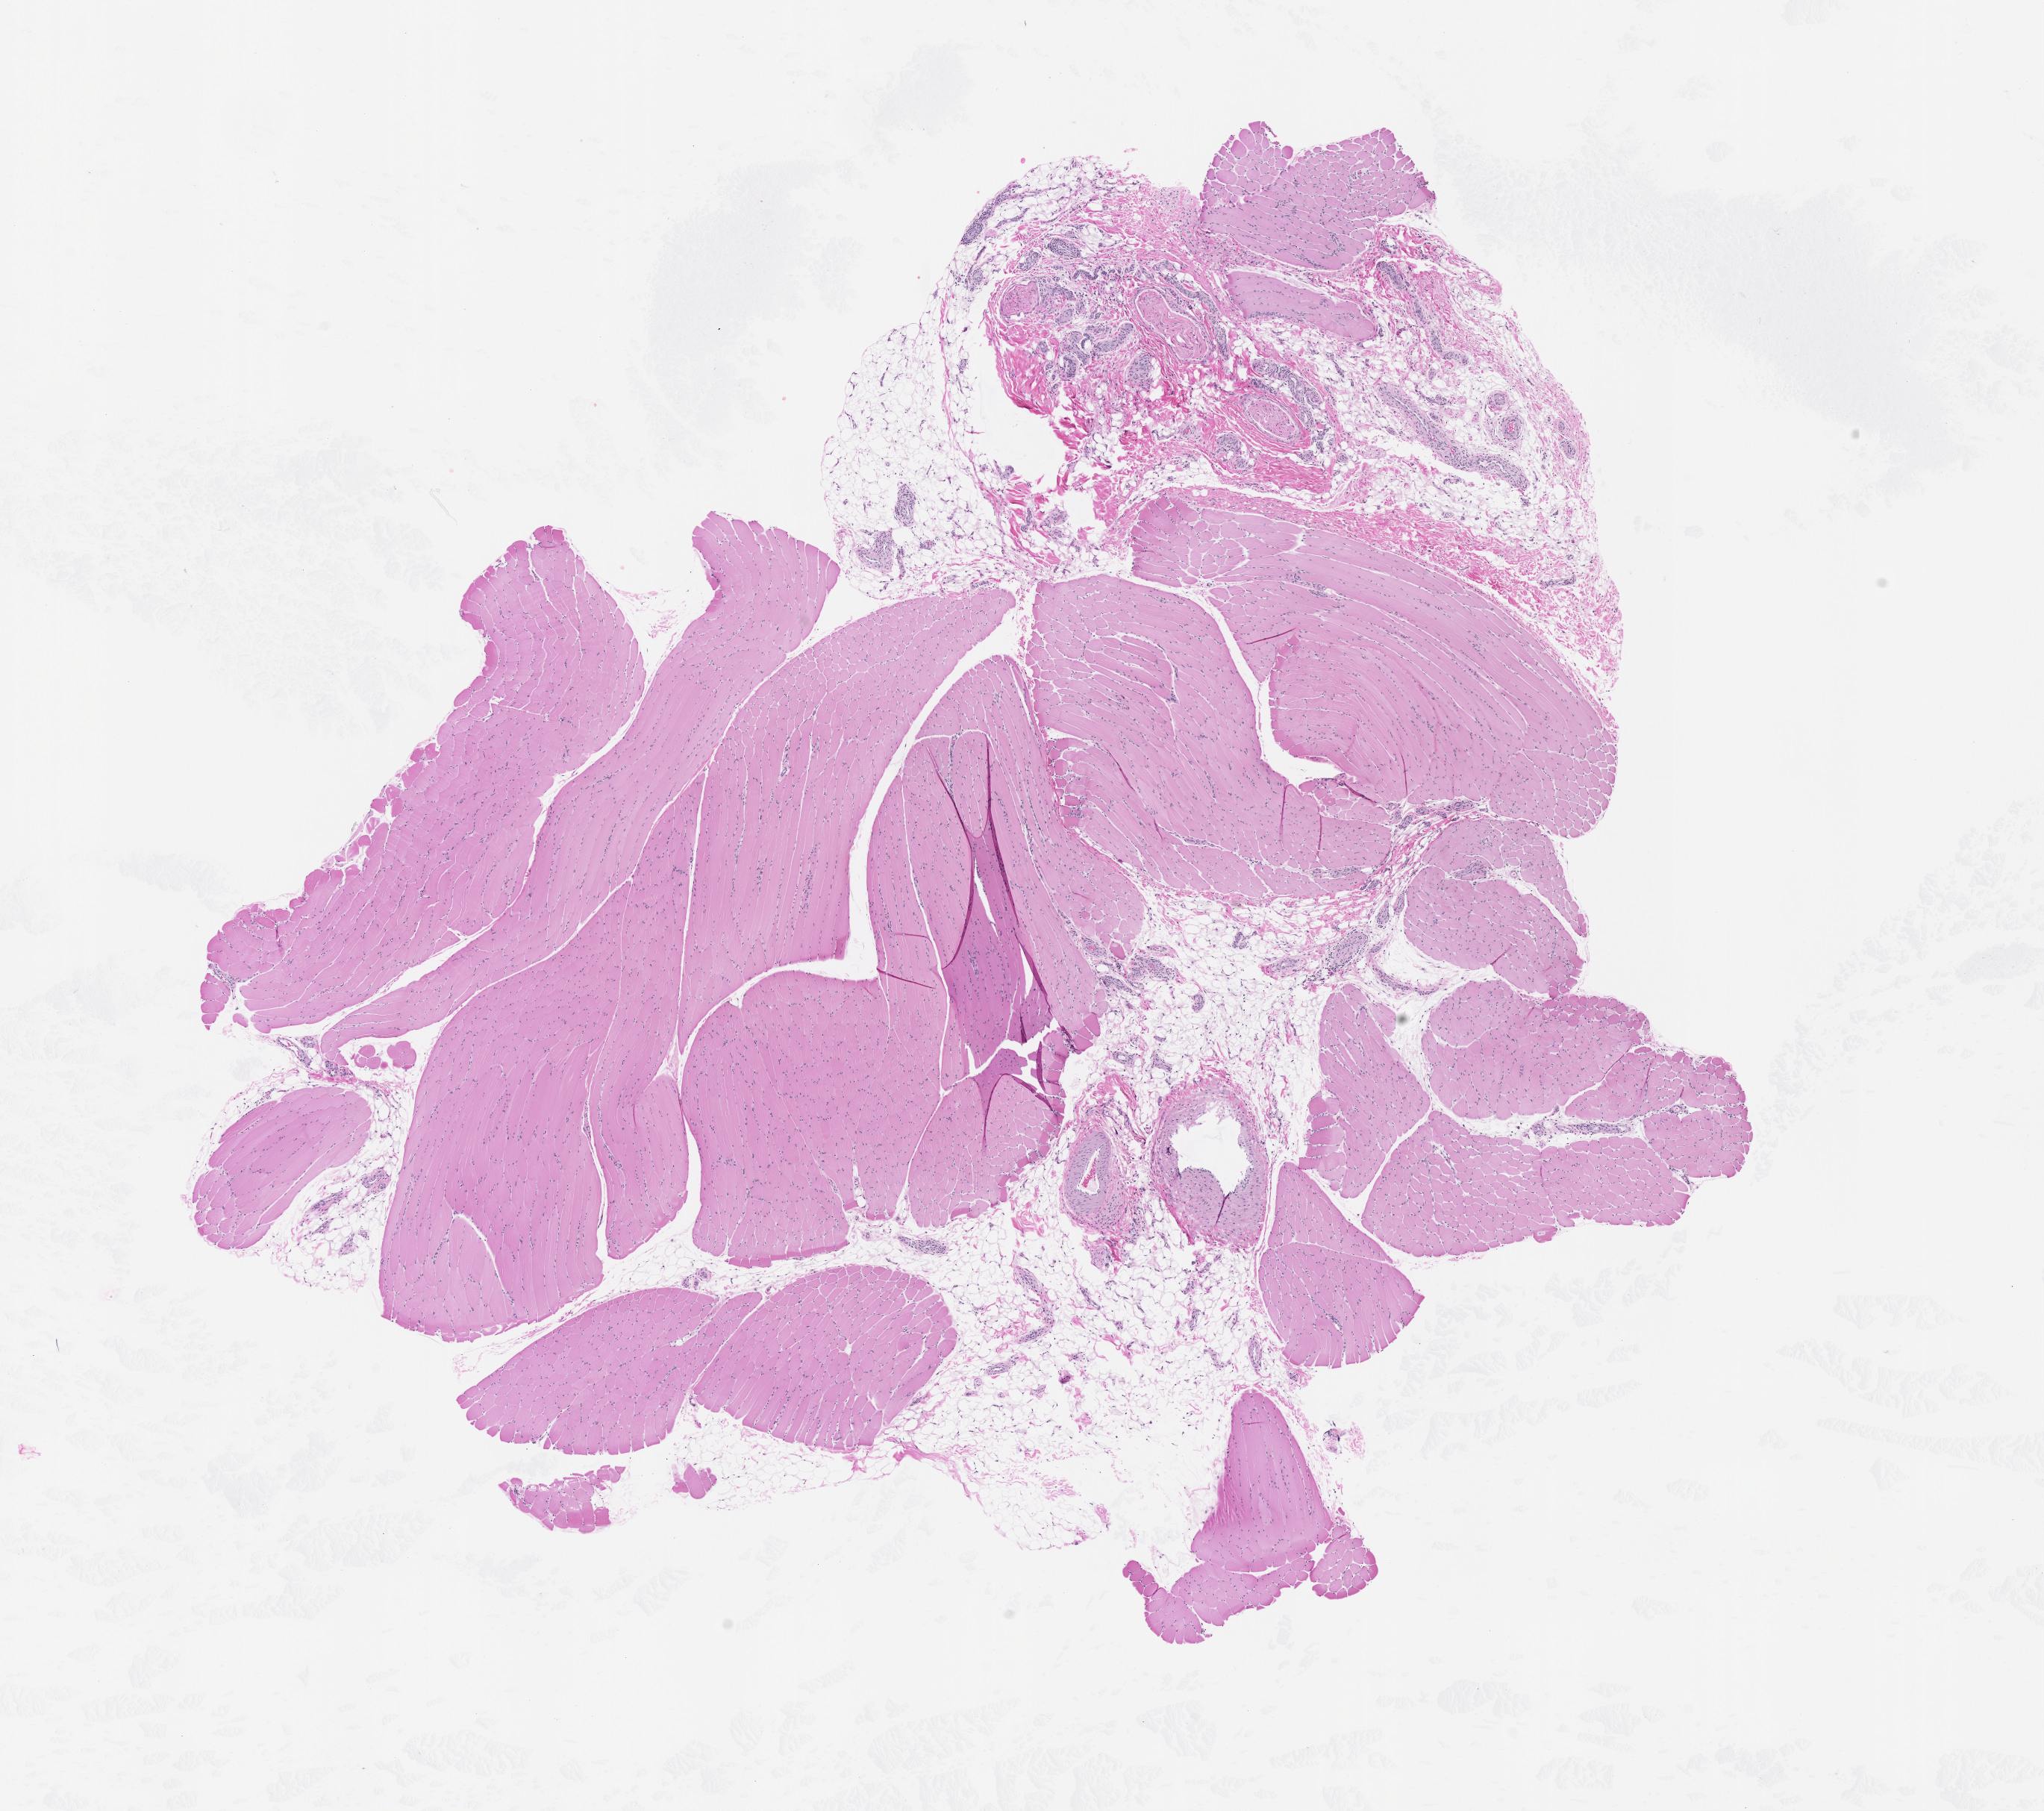
Digitized H&E-stained tissue section (whole slide), low-resolution overview of the scanned area, about 11.0 x 9.8 mm.
Patient diagnosis (cohort enrolment): sarcoma (site not recorded at cohort level).